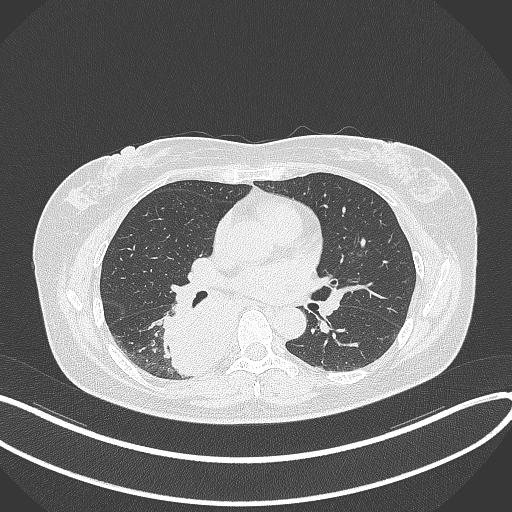
Chest CT, one axial slice. Slice 190 of 331 in the series (ordered by position). 120 kVp. Lung window (W 1500 / L -600 HU). 512 × 512 image matrix, field of view 400 × 400 mm. Female patient, age 54 years. Case-level facts recorded for this patient, not image findings: clinical TNM (as recorded): T4 N0 M0.
Annotated regions visible in this slice (rectangle marked by the reading radiologist):
- lung tumour (recorded histology: adenocarcinoma): bounding box <155,283,245,379> (left, top, right, bottom; pixels)